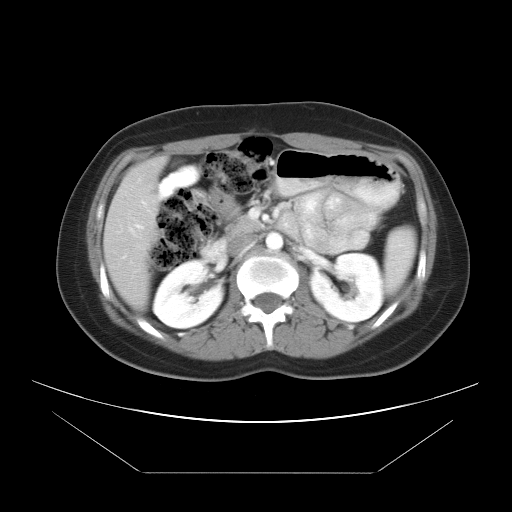
Contrast-enhanced abdominal CT, one axial slice; position 19 of 34 along the scan axis; reconstruction kernel STANDARD; 120 kVp; intravenous contrast given; soft-tissue window (W 400 / L 40 HU); 7.5 mm slice thickness; 512 × 512 image matrix, field of view 410 × 410 mm. Female patient, age 38 years. Case-level facts recorded for this patient, not image findings: diagnosis: colorectal cancer liver metastases, imaged before liver resection; multiple liver metastases: yes; largest metastasis: 3.1 cm; disease in both lobes: no.
Annotated regions visible in this slice (outlined manually by an expert reader):
- liver: bounding box [x1, y1, x2, y2] px = [104, 157, 166, 310]
- portal vein (with intrahepatic branches): [116, 206, 221, 260]
- liver metastasis: [149, 184, 160, 197]